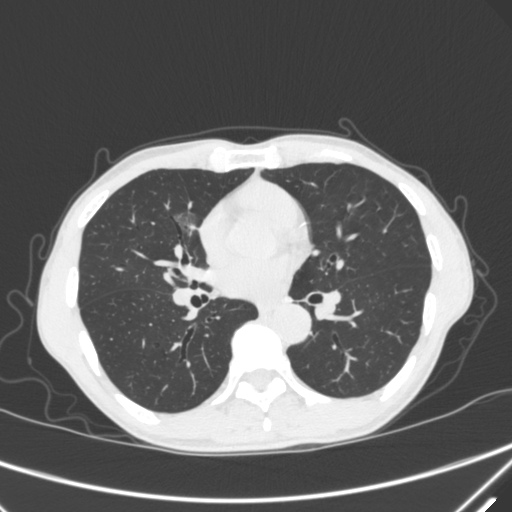
Chest CT, one axial slice. Position 169 of 340 along the scan axis. 120 kVp. Lung window (W 1500 / L -600 HU). 512 × 512 image matrix, field of view 350 × 350 mm. Male patient, age 67 years. From the clinical record (not read from this slice): clinical TNM (as recorded): T1c N0 M0; histopathological grade: G1-2.
Annotated regions visible in this slice (rectangle marked by the reading radiologist):
- lung tumour (recorded histology: adenocarcinoma): bounding box <169,202,198,247> (left, top, right, bottom; pixels)